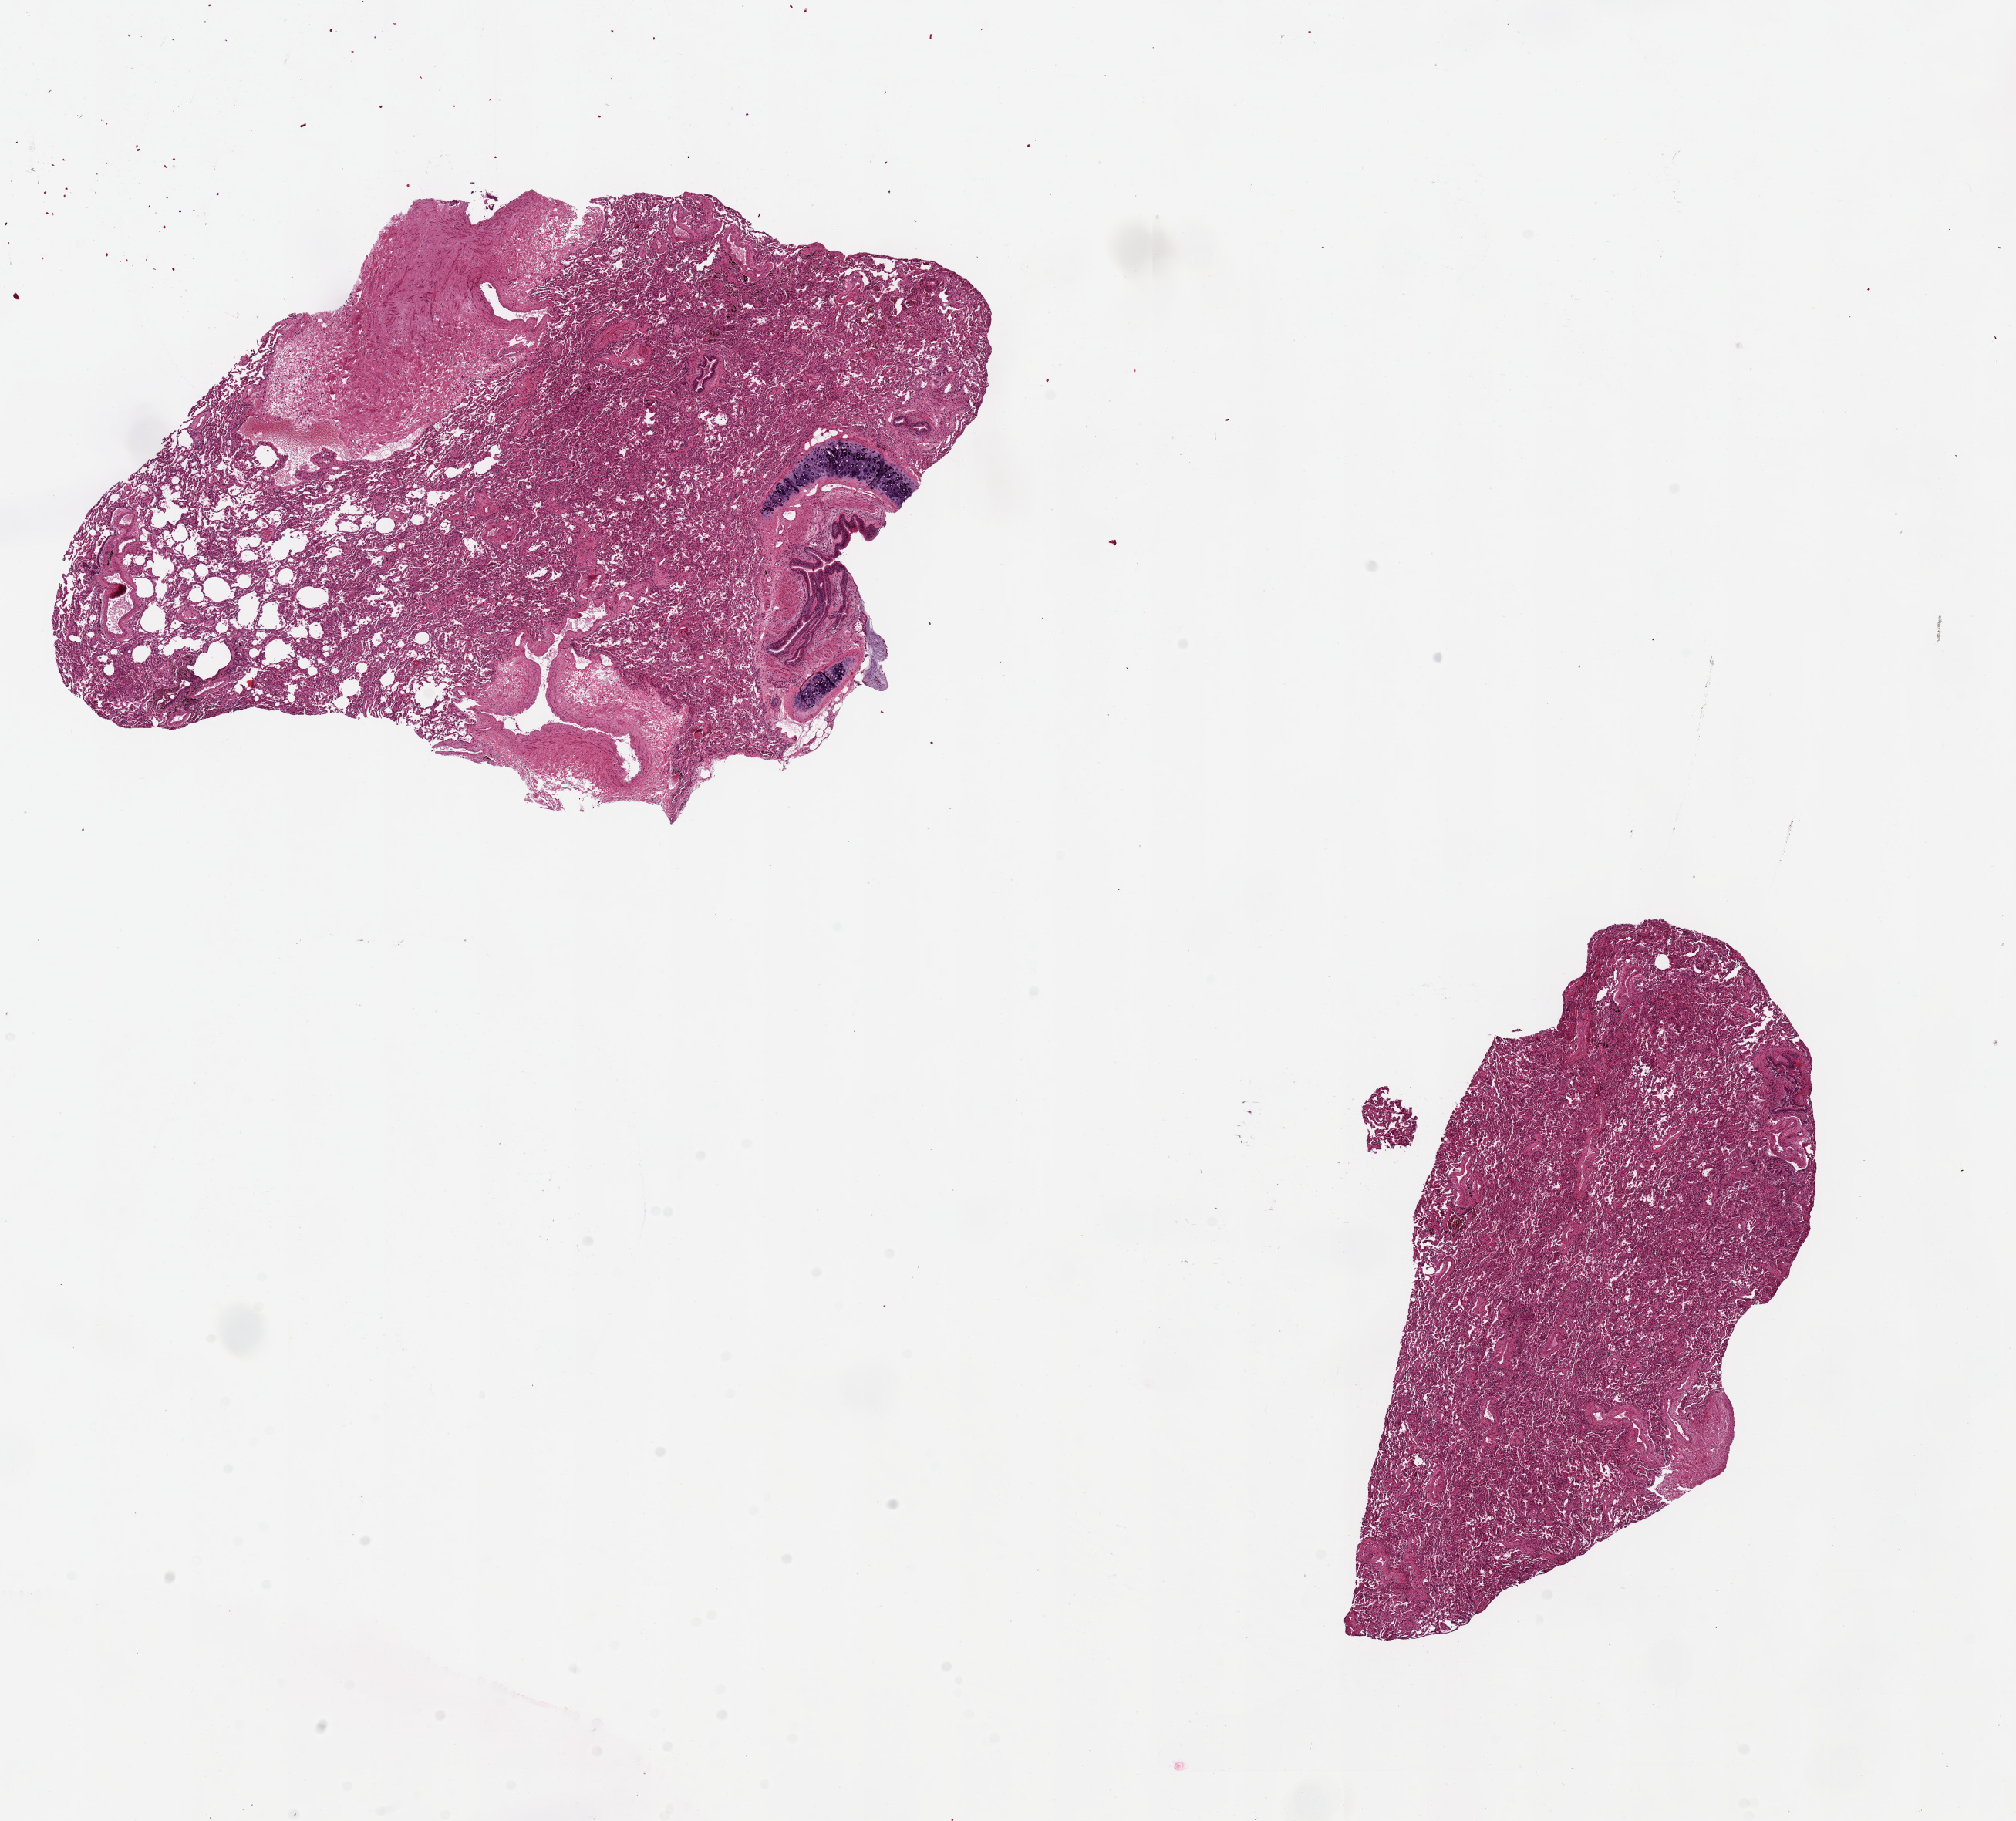
H&E whole-slide image — whole scanned area (about 20.7 x 18.7 mm, slide scanned at 20x) shown as a low-resolution overview; PAXgene-fixed paraffin-embedded (PFPE) section; sampled site (target tissue): lung; donor tissue sample. Donor sex: male.
Reviewer comment on this tissue sample: 2 pieces, 8.5x6.5 & 7.5x4mm; congested but well preserved.